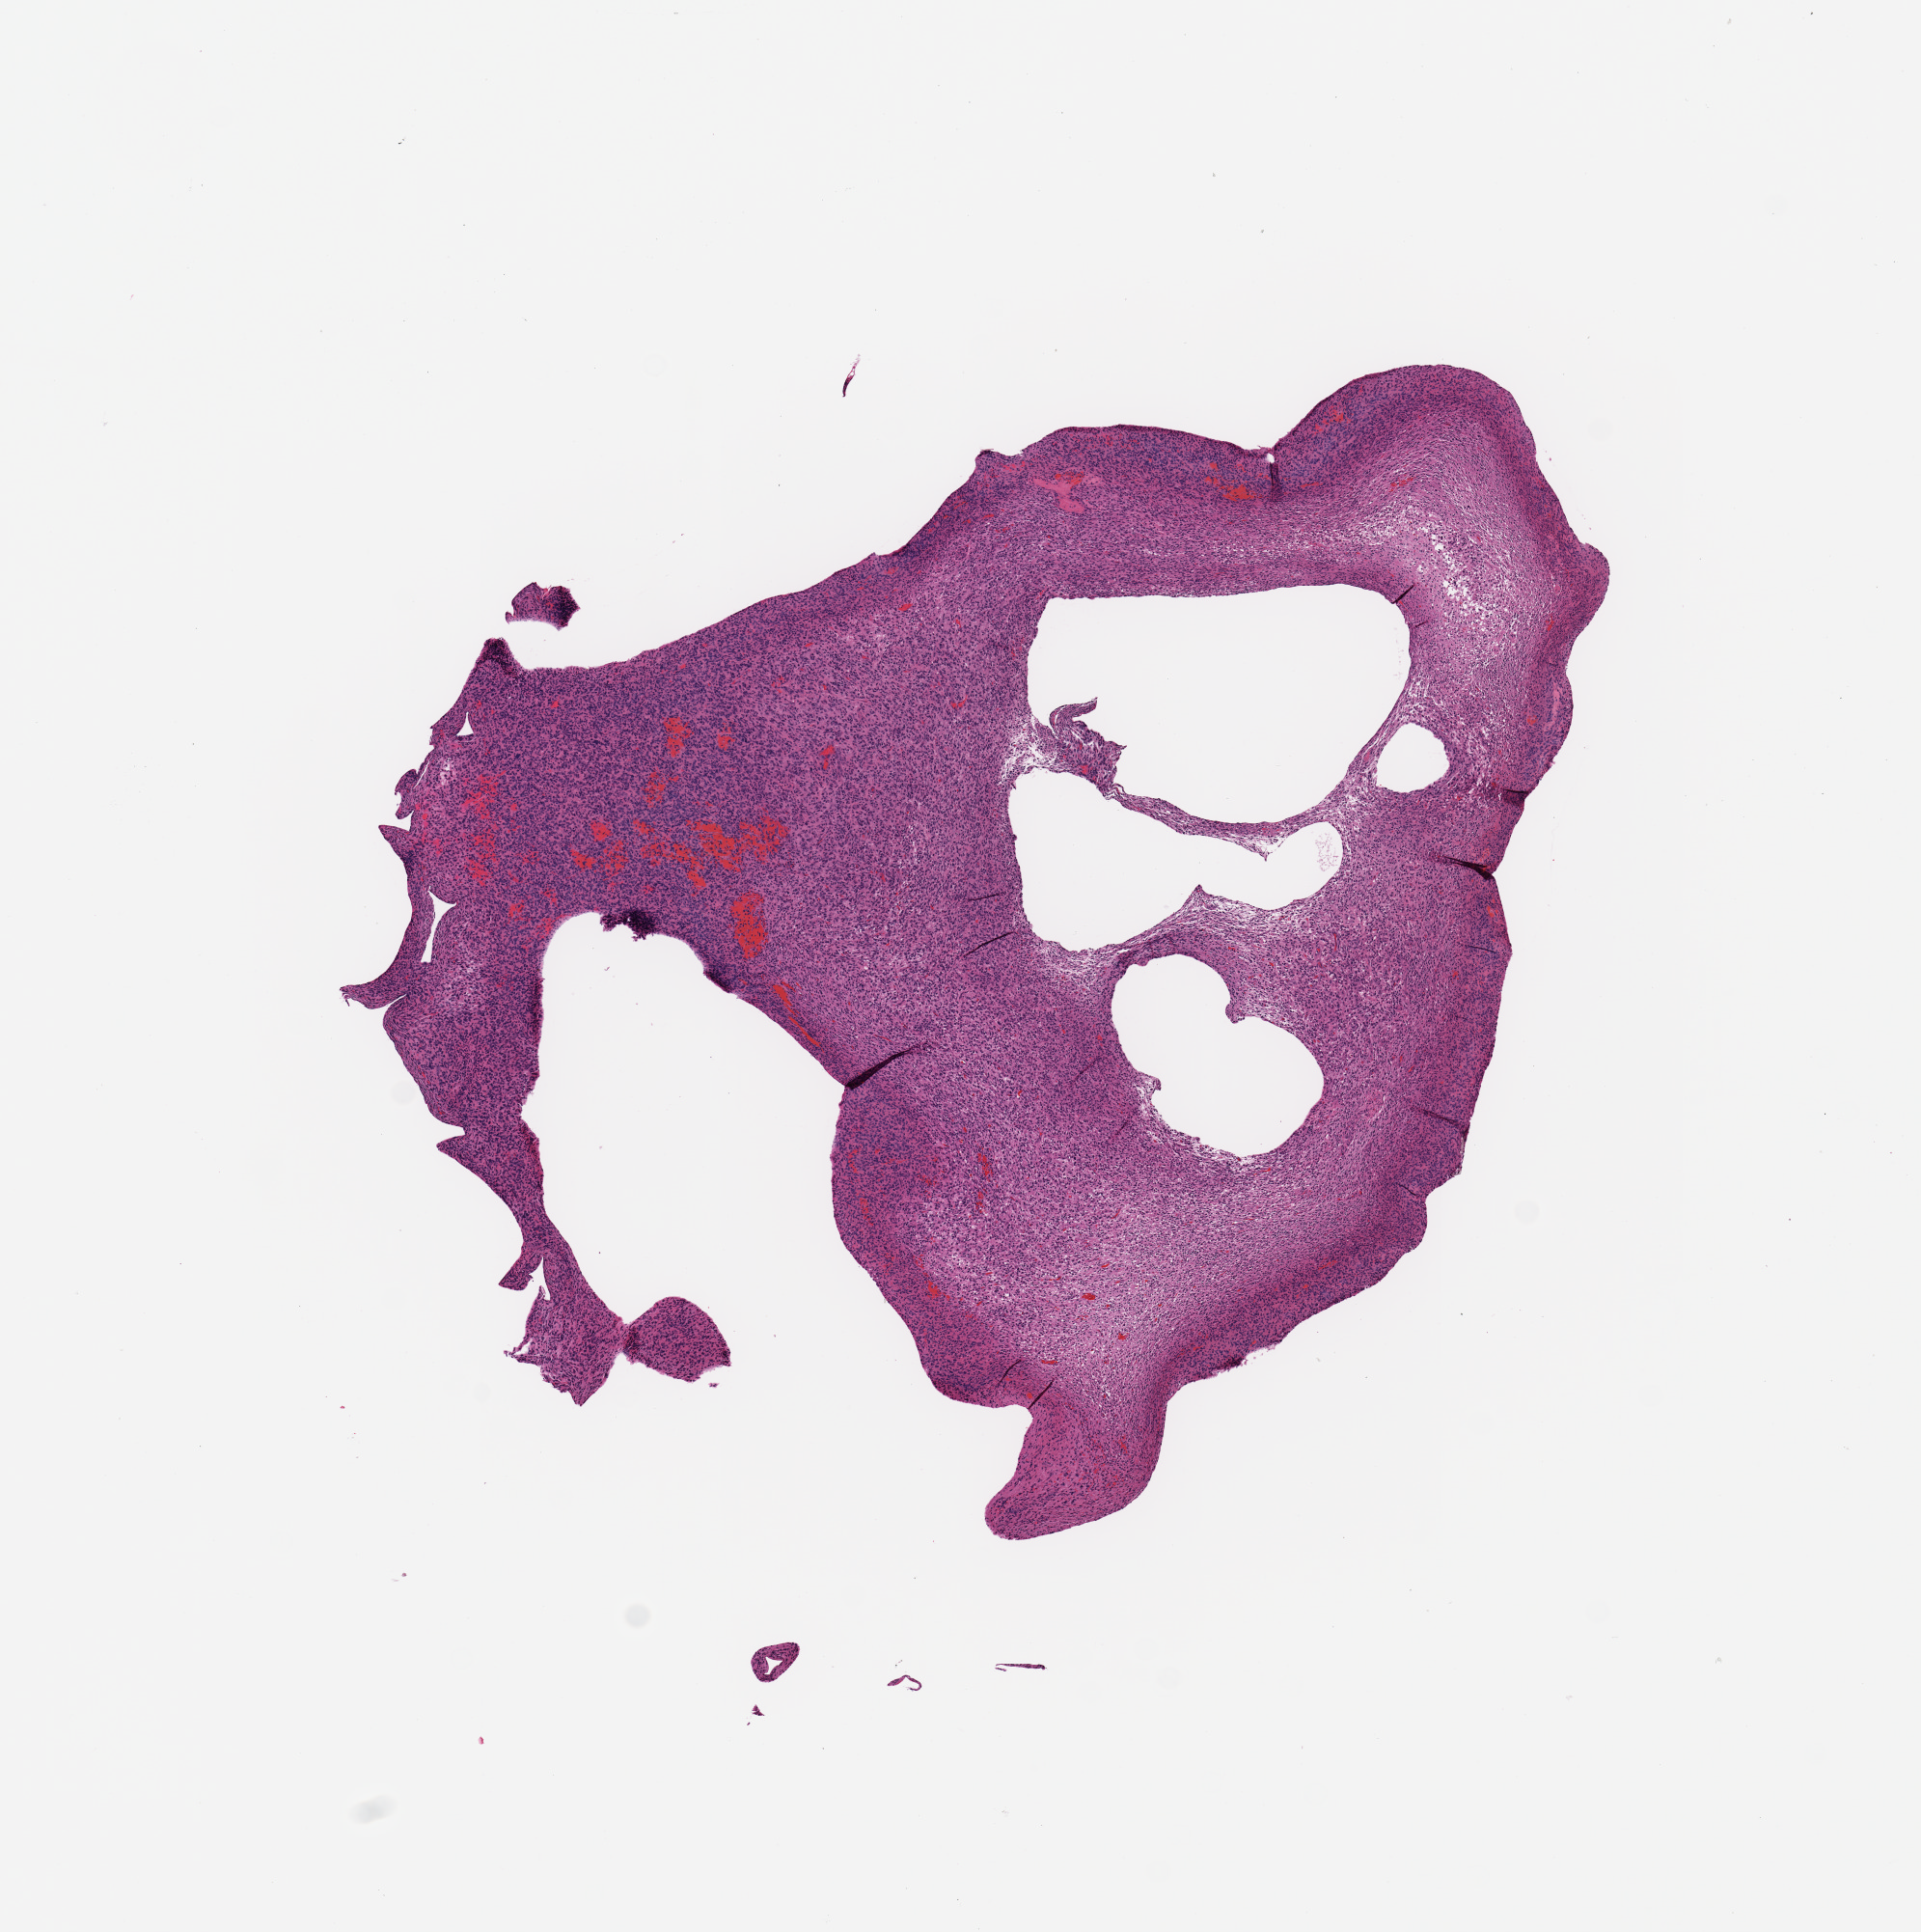
Digitized H&E tissue section (whole slide) — a low-resolution overview of the entire scanned area, about 7.9 x 7.9 mm (slide scanned at 20x). Tumour tissue sample, sampled site: frontal lobe. Patient: male, age 66 years. Composition of this section per pathologist review: tumour nuclei 90%, necrosis 0%.
Histologic diagnosis: Glioblastoma.